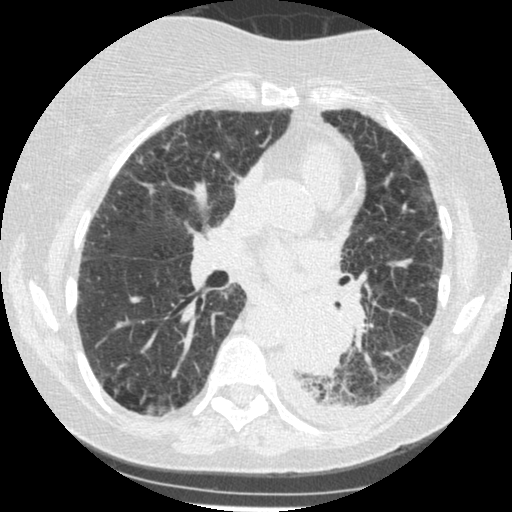
Chest CT (low-dose screening protocol), one axial image. Third annual screen. Lung window (W 1500 / L -600 HU). 1.25 mm slice thickness. 120 kVp. Female, age 60 years at enrolment. Former smoker at enrolment.
Expert reader's lesion annotation, box from (x=273, y=306) to (x=343, y=375) px. Screening reader's record for this exam (one nodule recorded; not confirmed to be the boxed lesion): non-calcified nodule or mass ≥4 mm, left lower lobe, 54 × 38 mm, smooth margins, soft tissue attenuation, pre-existing on the prior screen: yes; interval growth: yes. Official screen result: positive, other. Participant outcome: lung cancer diagnosed 15 days after this screen — small cell carcinoma, NOS, left lower lobe, undifferentiated (G4), stage IV (AJCC 6th edition), 69 mm at pathology.